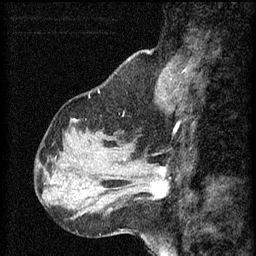
Breast MRI (dynamic contrast-enhanced), one sagittal slice; slice 19 of 60 in the series (ordered by position); 3 images stored at this slice position (order not interpretable as contrast timing); 1.5 T; TE 4.2 ms, TR 8.2 ms; 2 mm slice thickness; 256 × 256 image matrix. Female patient, age 37 years.
Outlined on this slice (semi-automatic segmentation, software-assisted and operator-edited):
- analysis volume of interest (the breast-tissue region the enhancement analysis was run in; not a lesion): bounding box (x1, y1, x2, y2) in pixels: (126, 156, 180, 203)
- tumour enhancement mask (voxels above the 70 % enhancement threshold inside the analysis volume of interest): (149, 168, 169, 199)